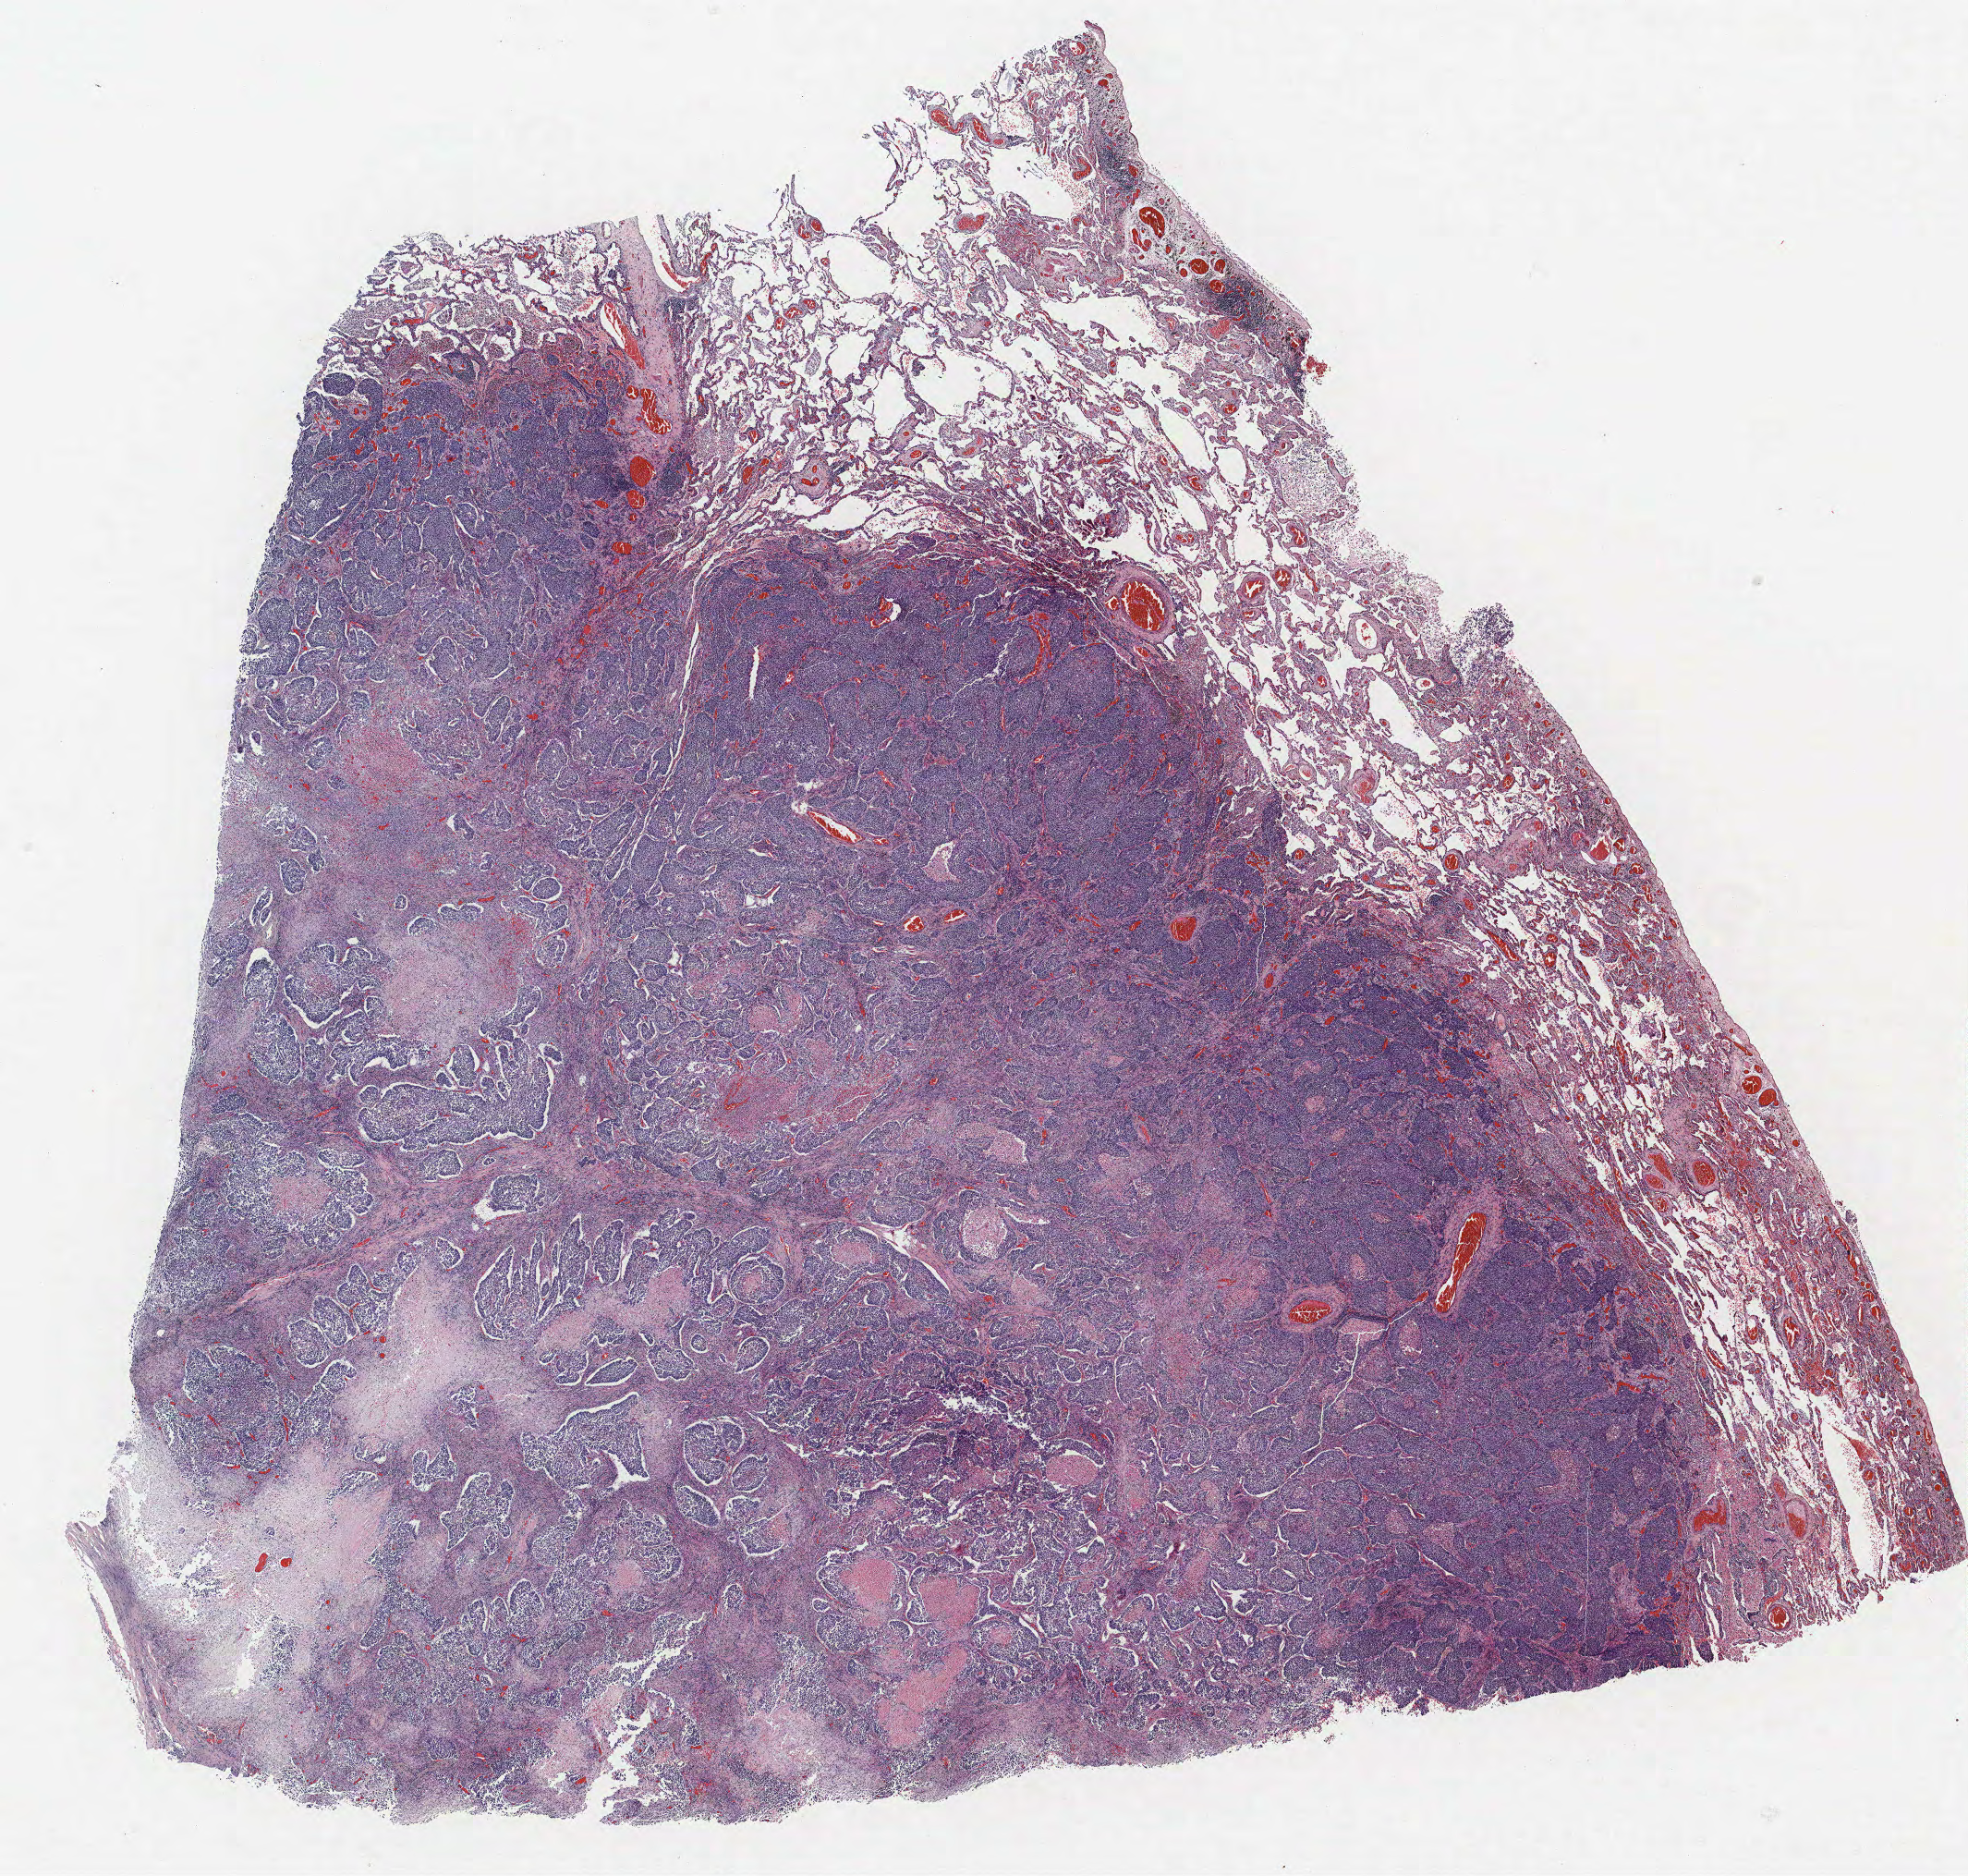
Whole-slide histology image, H&E, whole scanned area (about 17.0 x 16.2 mm) shown as a low-resolution overview. FFPE section. Lung. Male patient, aged 69 at enrolment. Current smoker at enrolment.
Participant's lung-cancer diagnosis: Squamous cell carcinoma, NOS (ICD-O-3 8070/3).